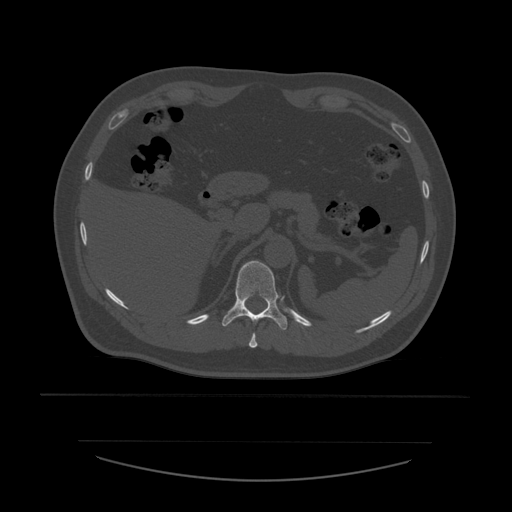
CT including the spine, one axial slice. Position 277 of 532 along the scan axis. Bone window (W 1800 / L 400 HU). 512 × 512 image matrix, field of view 441 × 441 mm. Patient age 44 years. Case-level facts recorded for this patient, not image findings: primary cancer: soft tissue sarcoma.
Annotated regions visible in this slice (semi-automatically segmented with operator editing):
- T10 vertebra: bounding box <249,333,258,348> (left, top, right, bottom; pixels)
- T11 vertebra: <222,261,288,331>